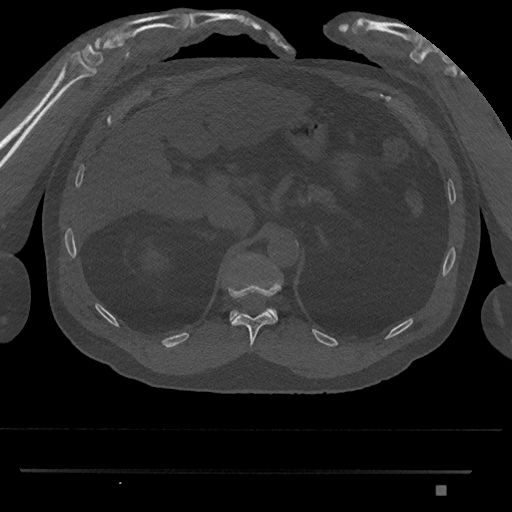
CT including the spine, one axial slice. Slice 929 of 1134 in the series (ordered by position). Bone window (W 1800 / L 400 HU). 512 × 512 image matrix, field of view 429 × 429 mm. Male patient, age 65 years. Case-level facts recorded for this patient, not image findings: primary cancer: prostate.
Structures marked on this image (semi-automatic segmentation, software-assisted and operator-edited):
- T11 vertebra: bounding box <227,280,282,349> (left, top, right, bottom; pixels)
- T12 vertebra: <229,255,278,322>